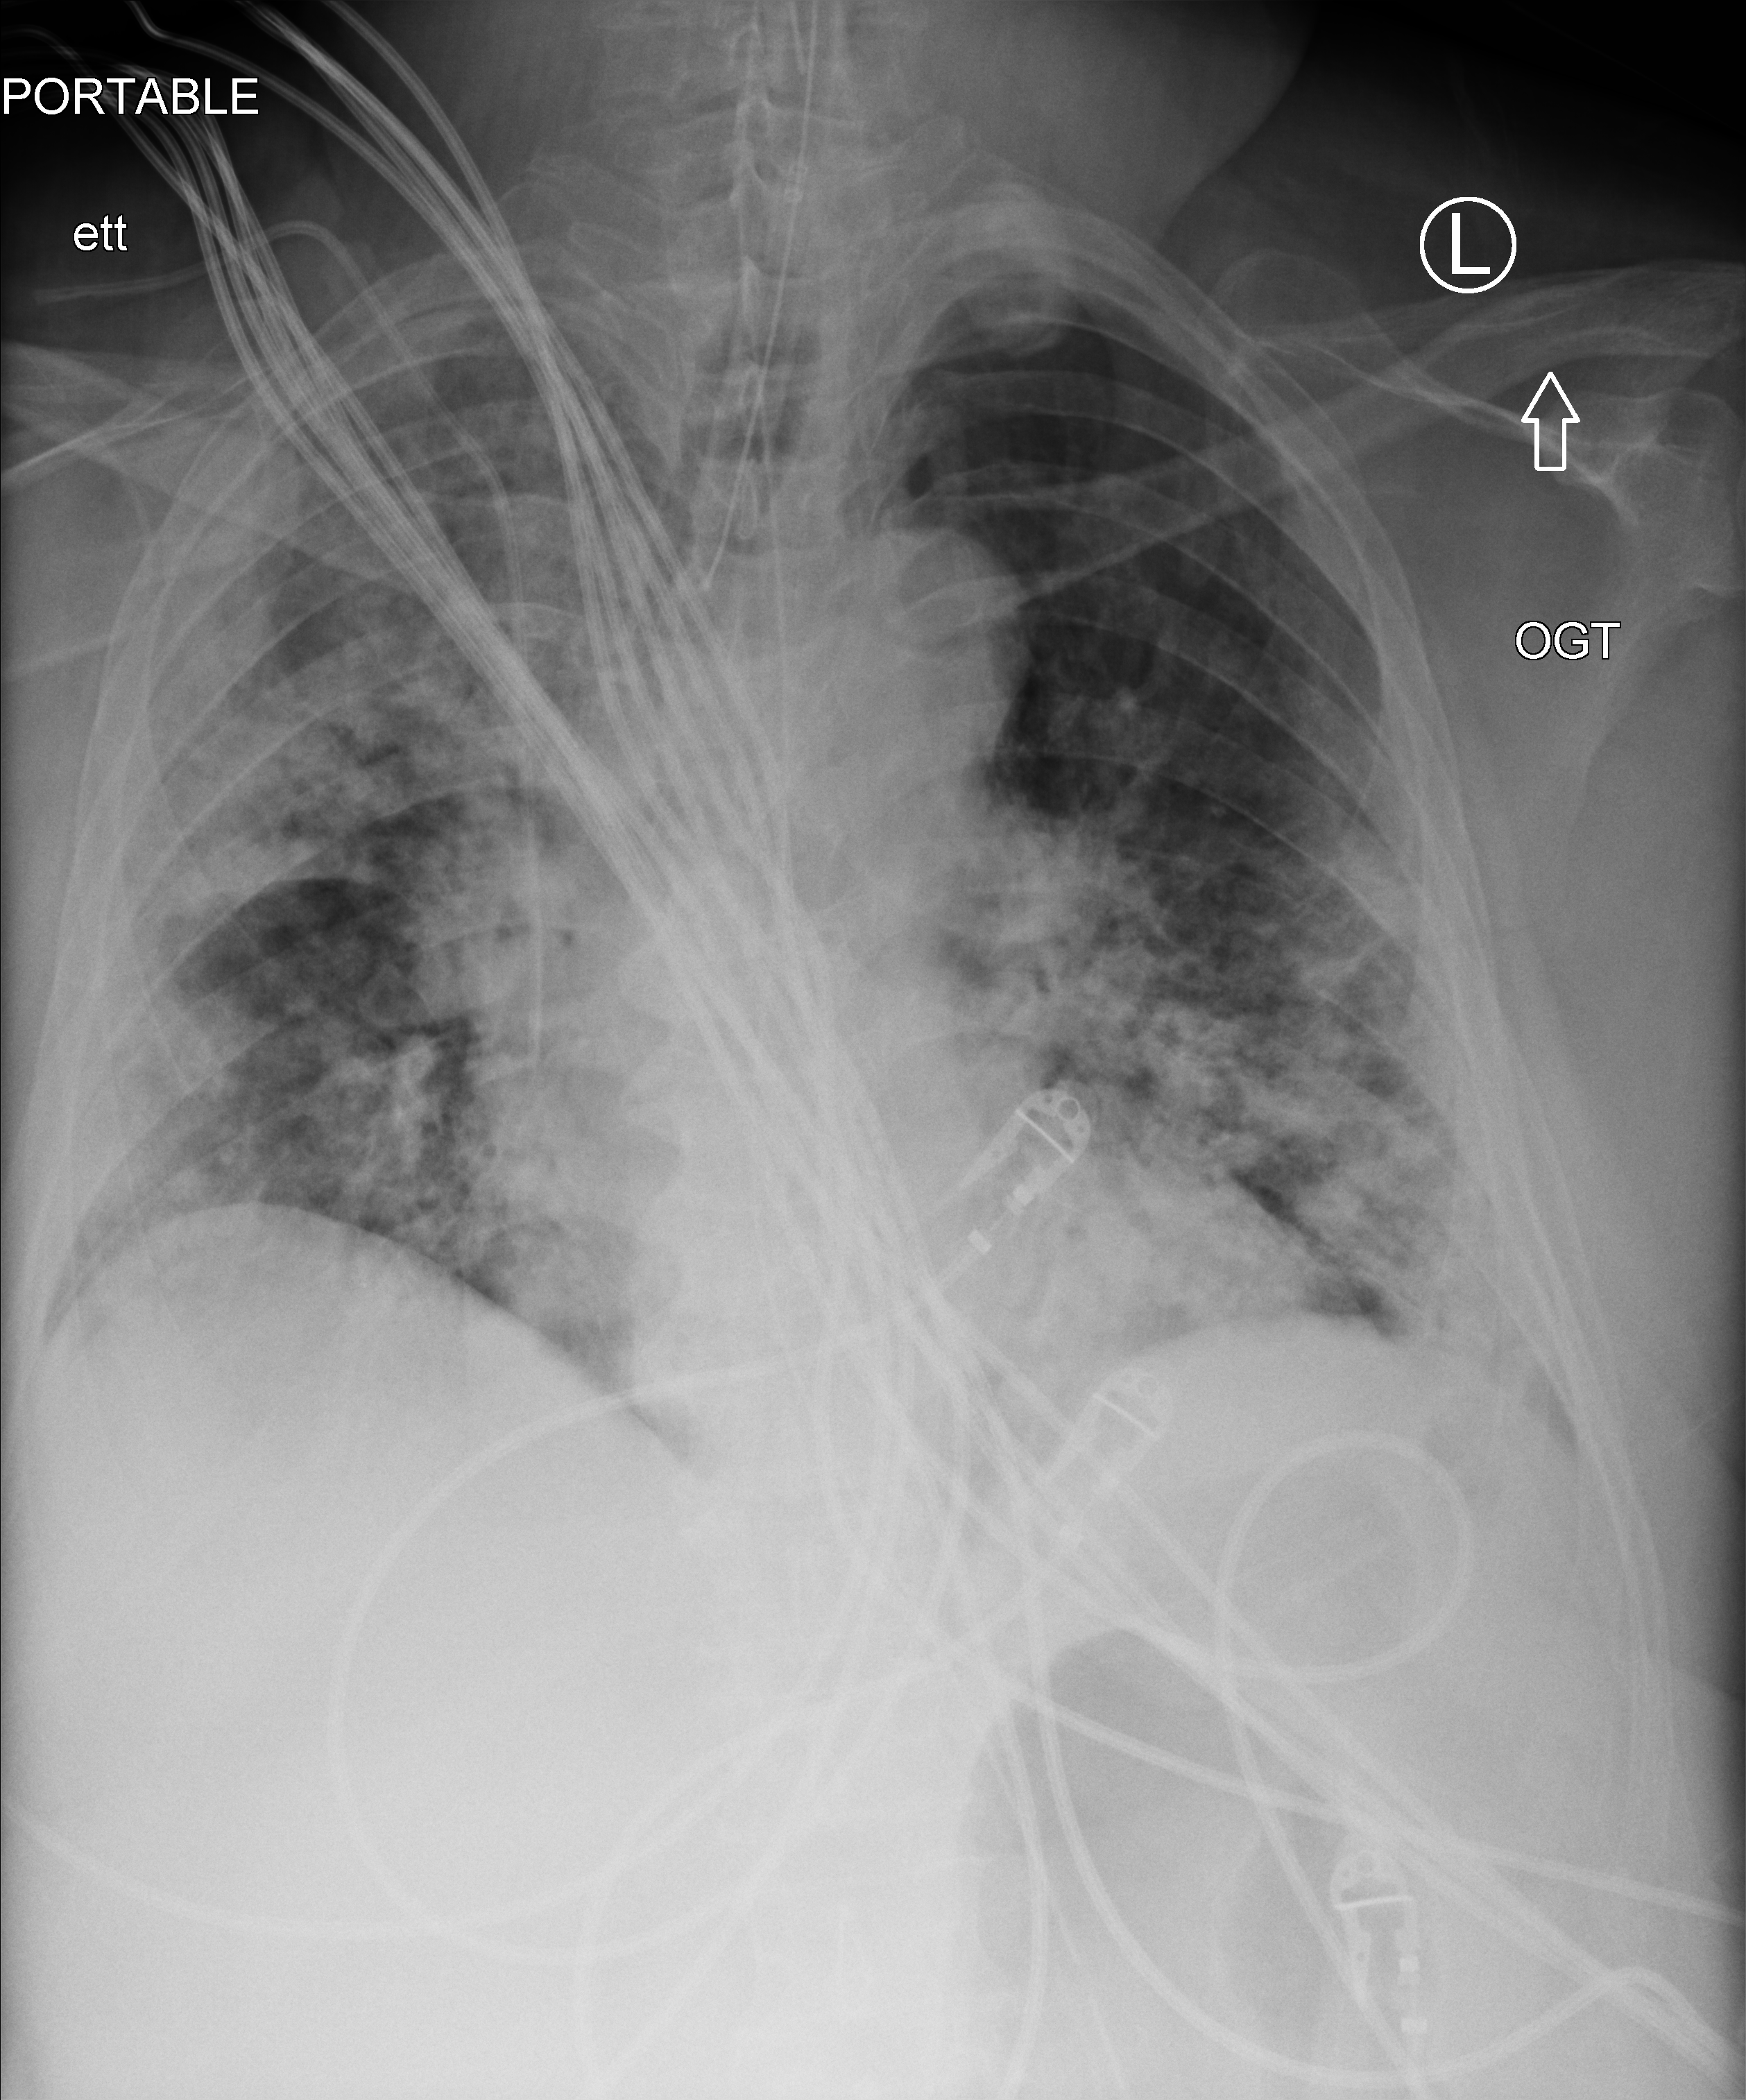
Portable chest radiograph; anteroposterior (AP) projection. Patient hospitalised with COVID-19, aged 18–59 years.
From the hospital-stay record, not from the radiograph (when in the stay this image was taken is not recorded):
- length of hospital stay: 28 days
- admitted to intensive care during this hospital stay: yes
- COPD (admission record): no